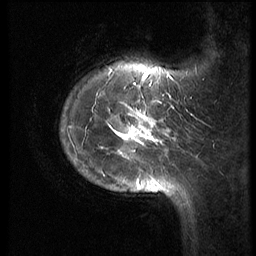
Breast MRI (dynamic contrast-enhanced), one sagittal slice; position 13 of 70 along the scan axis; 3 images stored at this slice position (order not interpretable as contrast timing); 1.5 T; TE 4.2 ms, TR 9 ms; 256 × 256 image matrix, field of view 180 × 180 mm. Patient: female, 28 years. From the clinical record (not read from this slice): setting: breast cancer imaged before/during neoadjuvant chemotherapy.
Outlined on this slice (semi-automatic segmentation, software-assisted and operator-edited):
- analysis volume of interest (the breast-tissue region the enhancement analysis was run in; not a lesion): bounding box (x1, y1, x2, y2) in pixels: (63, 48, 186, 215)
- tumour enhancement mask (voxels above the 140 % enhancement threshold inside the analysis volume of interest): (76, 75, 176, 194)